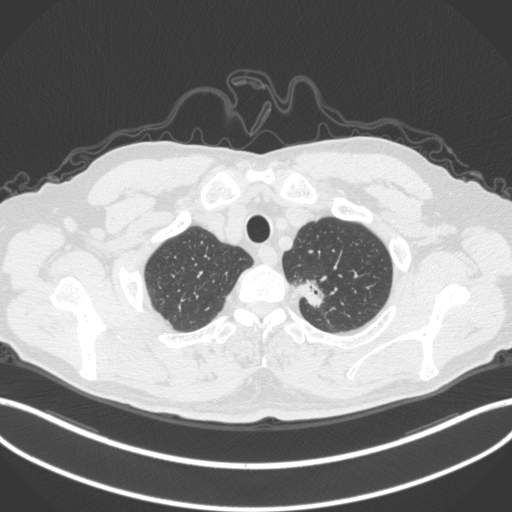
Chest CT, one axial slice; position 338 of 382 along the scan axis; 120 kVp; lung window (W 1500 / L -600 HU); 512 × 512 image matrix, field of view 400 × 400 mm. Patient: male, 64 years. Case-level facts recorded for this patient, not image findings: clinical TNM (as recorded): T1c N0 M0.
Outlined on this slice (bounding box drawn by a radiologist):
- lung tumour (recorded histology: adenocarcinoma): box from (x=292, y=274) to (x=333, y=315) px